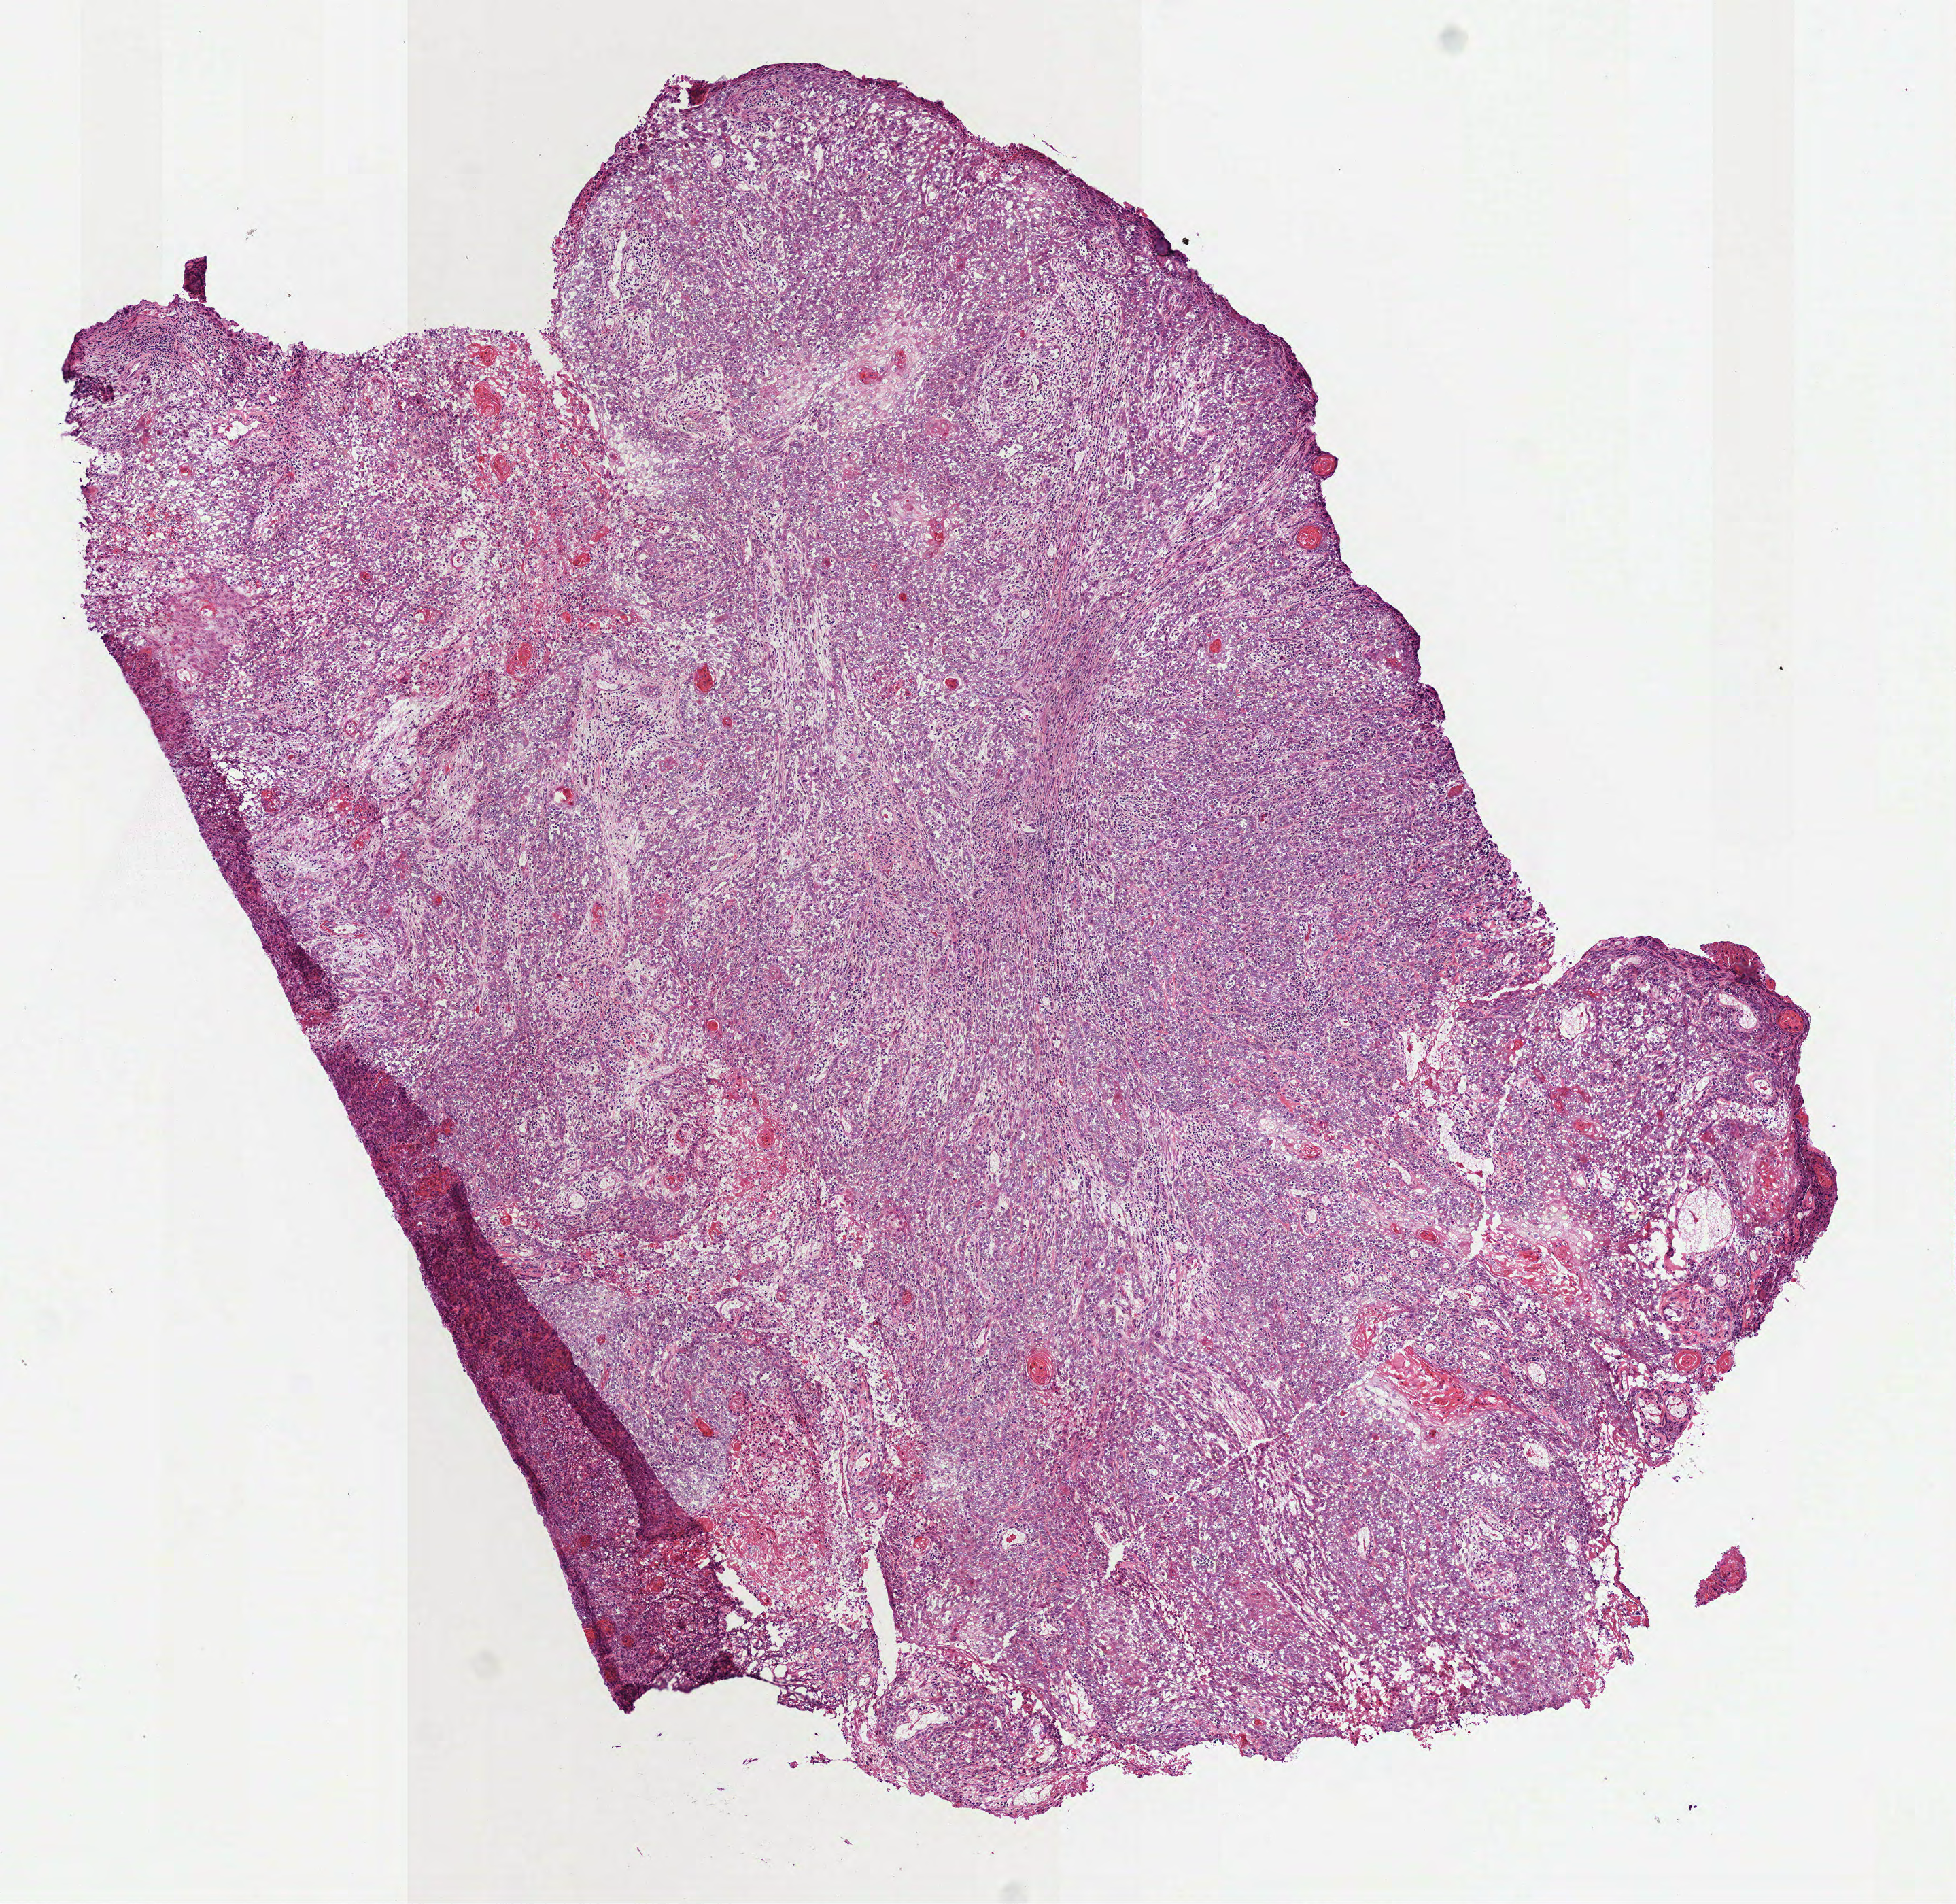
Whole-slide histology image, H&E, whole scanned area (about 5.8 x 5.6 mm, acquisition: 40x scan) shown as a low-resolution overview. Frozen section from the bottom of the tissue portion. Head and neck, primary tumour sample. Male patient; age at initial diagnosis 54 years. Histologic grade: GX (grade cannot be assessed). Slide review estimates, as recorded: tumour cells 95%, tumour nuclei 70%, normal cells 0%, stromal cells 5%, necrosis 0%.
* TNM: T4a N1 M0
* lymph nodes positive (case pathology): 1 of 43 examined
* histologic diagnosis: Squamous cell carcinoma, keratinizing, NOS (cheek mucosa)
* AJCC pathologic stage: IVA